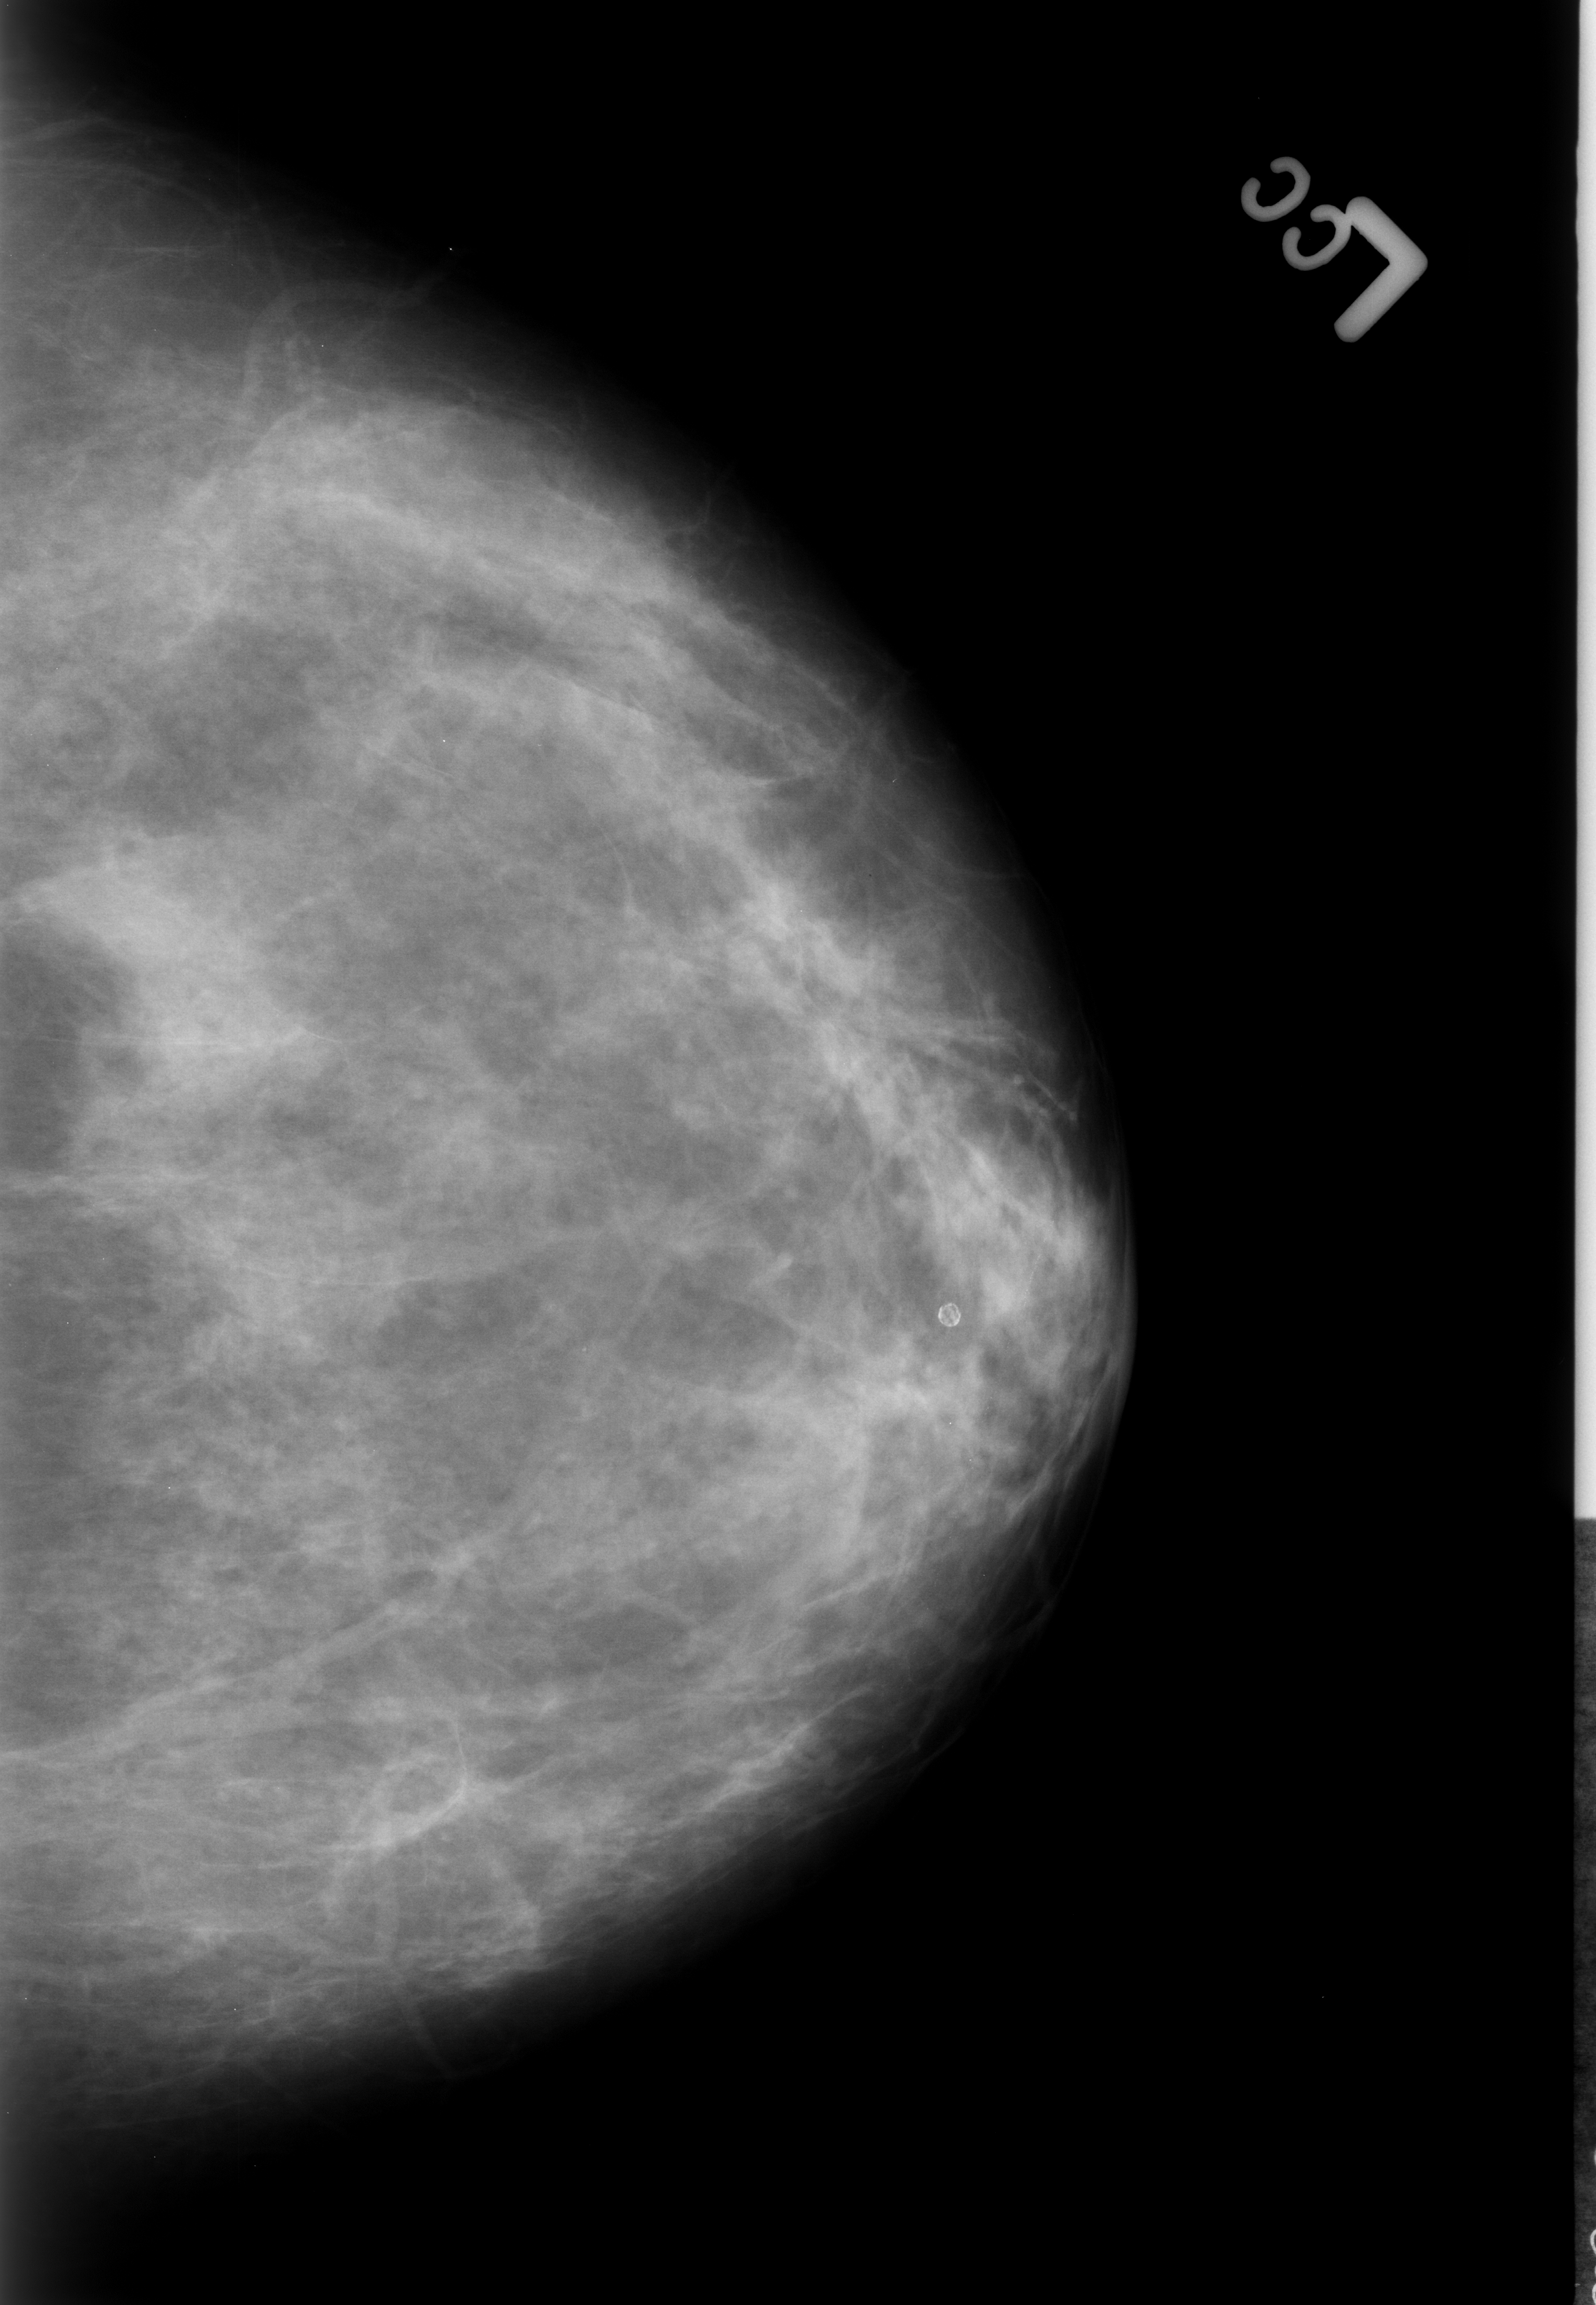
Scanned film-screen mammogram. Left breast. CC view. BI-RADS breast density category 2 (scale 1–4). 1596 × 2305 image matrix.
Expert-marked regions of interest on this image (one box per marked abnormality):
- calcifications, morphology lucent center; BI-RADS assessment category 2; subtlety rating 5 on a 1 (subtle) to 5 (obvious) scale; outcome (as recorded, no biopsy): benign without callback (not worked up further): box from (x=854, y=1350) to (x=939, y=1427) px